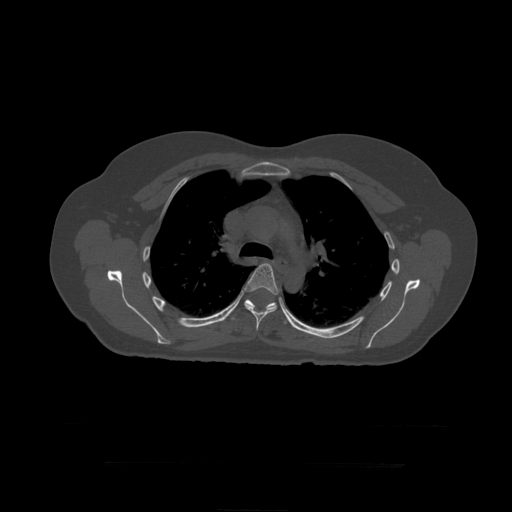
CT including the spine, one axial slice. Slice 315 of 399 in the series (ordered by position). Bone window (W 1800 / L 400 HU). 512 × 512 image matrix, field of view 450 × 450 mm. Patient age 41 years. From the clinical record (not read from this slice): primary cancer: breast.
Outlined on this slice (semi-automatic segmentation, software-assisted and operator-edited):
- T6 vertebra: box from (x=244, y=264) to (x=279, y=331) px
- T7 vertebra: (x=232, y=300)–(x=287, y=325)